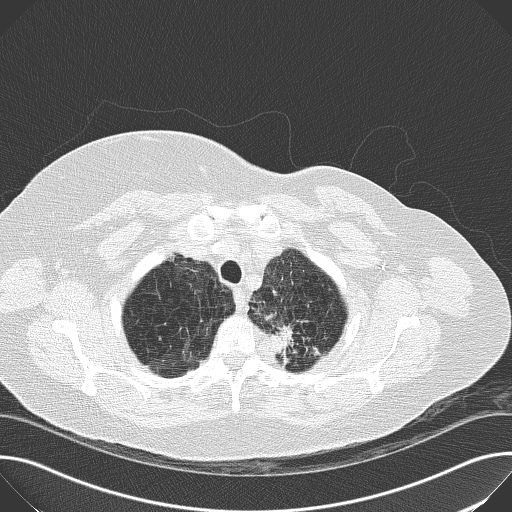
Low-dose screening chest CT, one axial slice; position 147 of 169 along the scan axis; reconstruction kernel B50f; 120 kVp; lung window (W 1500 / L -600 HU); 2 mm slice thickness; 512 × 512 image matrix, field of view 380 × 380 mm.
Structures marked on this image (expert manual segmentation):
- lesion 1 (tumor, upper lobe of left lung): box from (x=265, y=325) to (x=294, y=364) px